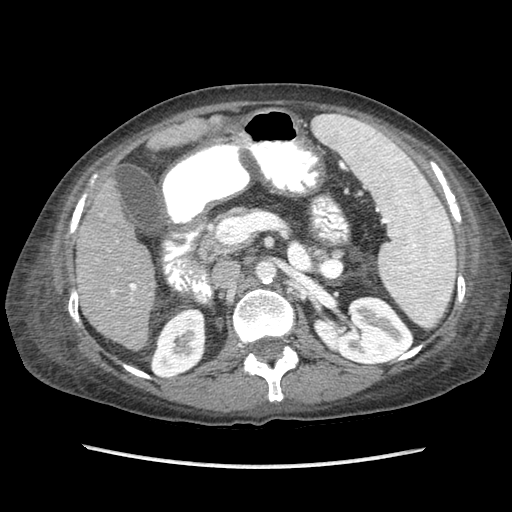
Contrast-enhanced abdominal CT (liver protocol), one axial slice. Slice 34 of 87 in the series (ordered by position). Soft-tissue window (W 400 / L 40 HU). 2.5 mm slice thickness. 512 × 512 image matrix, field of view 340 × 340 mm. From the clinical record (not read from this slice): diagnosis: hepatocellular carcinoma (patient treated with transarterial chemoembolisation; whether this scan precedes or follows treatment is not stated here); TNM stage (as recorded): Stage-IIIB; Child-Pugh class: A; tumour differentiation: no biopsy; tumour nodularity: uninodular.
Annotated regions visible in this slice (semi-automatically segmented with operator editing):
- liver parenchyma outside the tumour (the mass and vessels are separate outlines, so this box may not span the whole liver): box from (x=76, y=116) to (x=220, y=350) px
- liver vessels: (x=111, y=283)–(x=137, y=301)